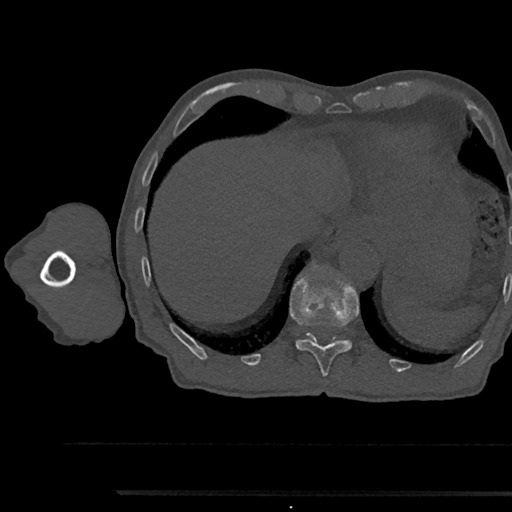
CT including the spine, one axial slice. Position 772 of 797 along the scan axis. Reconstruction kernel Br40s/3. Bone window (W 1800 / L 400 HU). 0.5 mm slice thickness. 512 × 512 image matrix, field of view 367 × 367 mm. Male patient, age 79 years. From the clinical record (not read from this slice): primary cancer: prostate.
Outlined on this slice (semi-automatically segmented with operator editing):
- T11 vertebra: bounding box (x1, y1, x2, y2) in pixels: (290, 278, 358, 379)